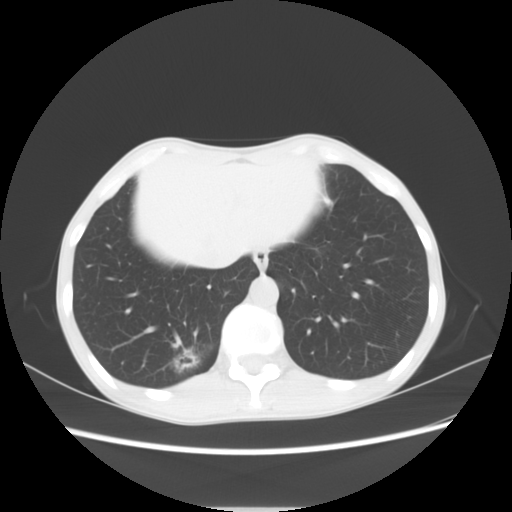
Chest CT, one axial slice; position 17 of 69 along the scan axis; reconstruction kernel STANDARD; lung window (W 1500 / L -600 HU); 512 × 512 image matrix. Patient: female, 51 years. From the clinical record (not read from this slice): clinical TNM (as recorded): T1c N0 M0; histopathological grade: G2-3.
Outlined on this slice (rectangle marked by the reading radiologist):
- lung tumour (recorded histology: adenocarcinoma): bounding box <162,334,220,381> (left, top, right, bottom; pixels)